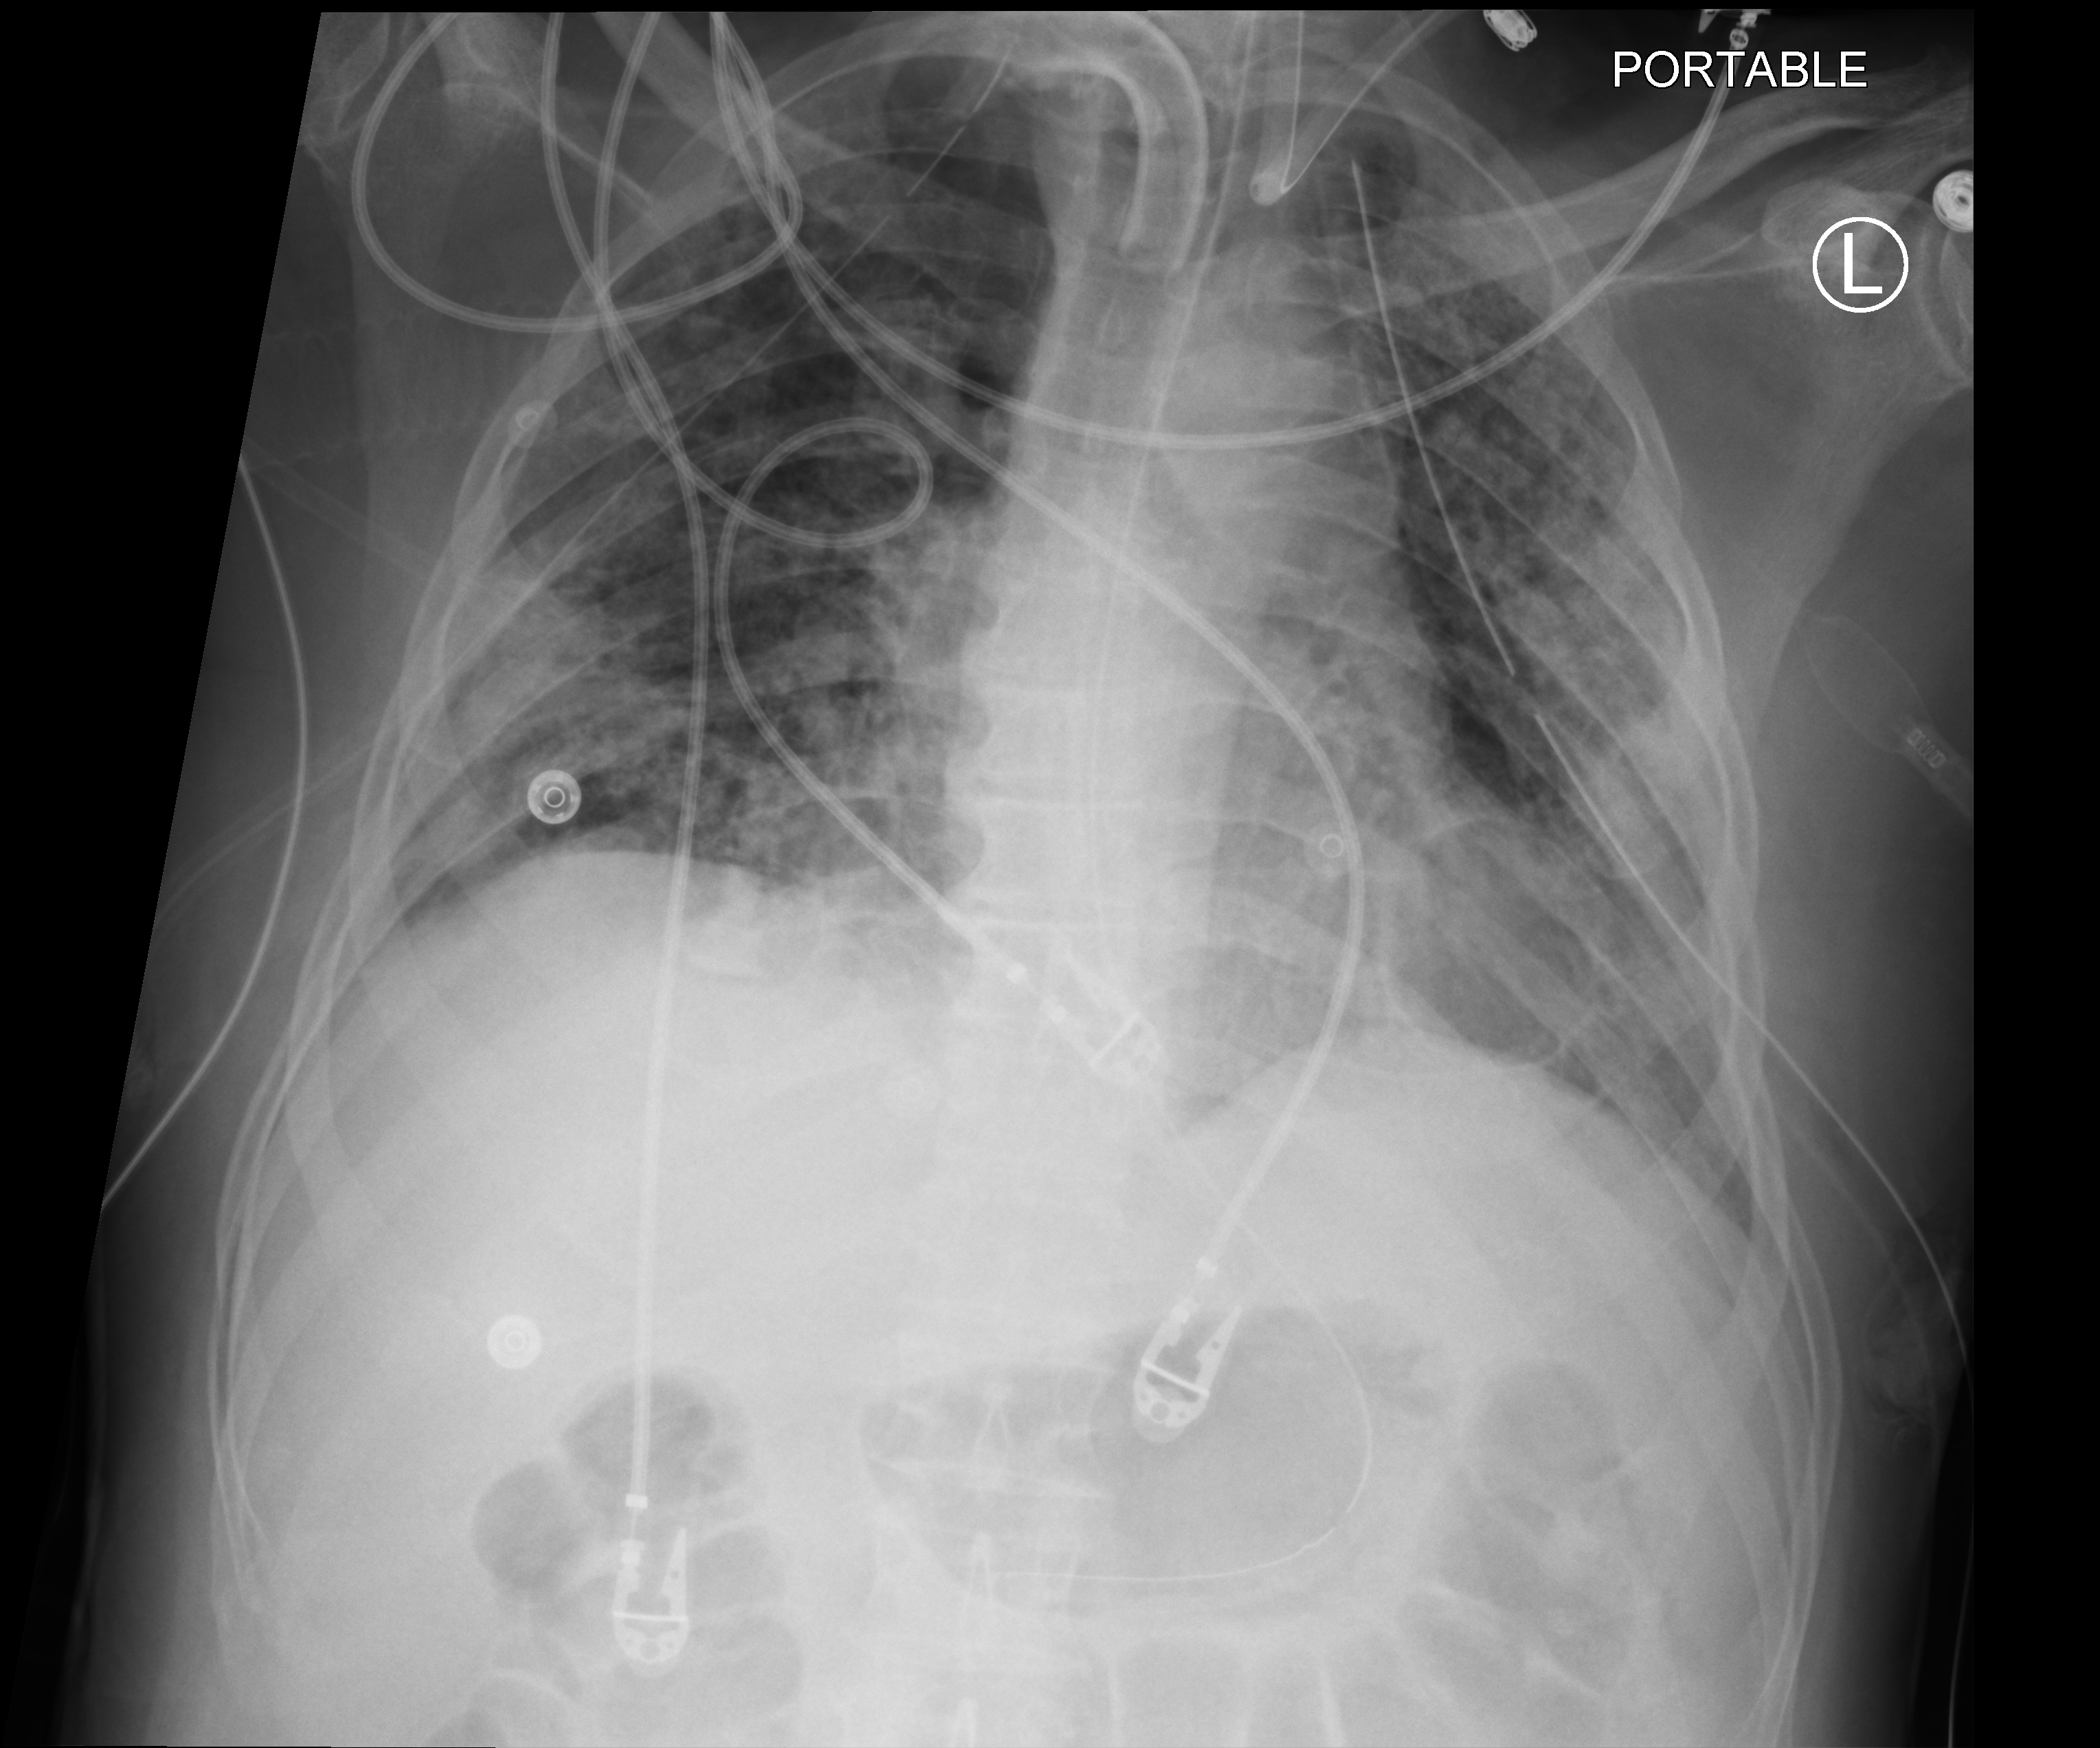
Bedside chest radiograph (computed radiography); anteroposterior (AP) projection. Patient hospitalised with COVID-19; male, aged 18–59 years.
Hospital-stay facts (about this admission, not read from this image; timing relative to this image not recorded): length of hospital stay: 83 days; mechanically ventilated during this hospital stay: yes.